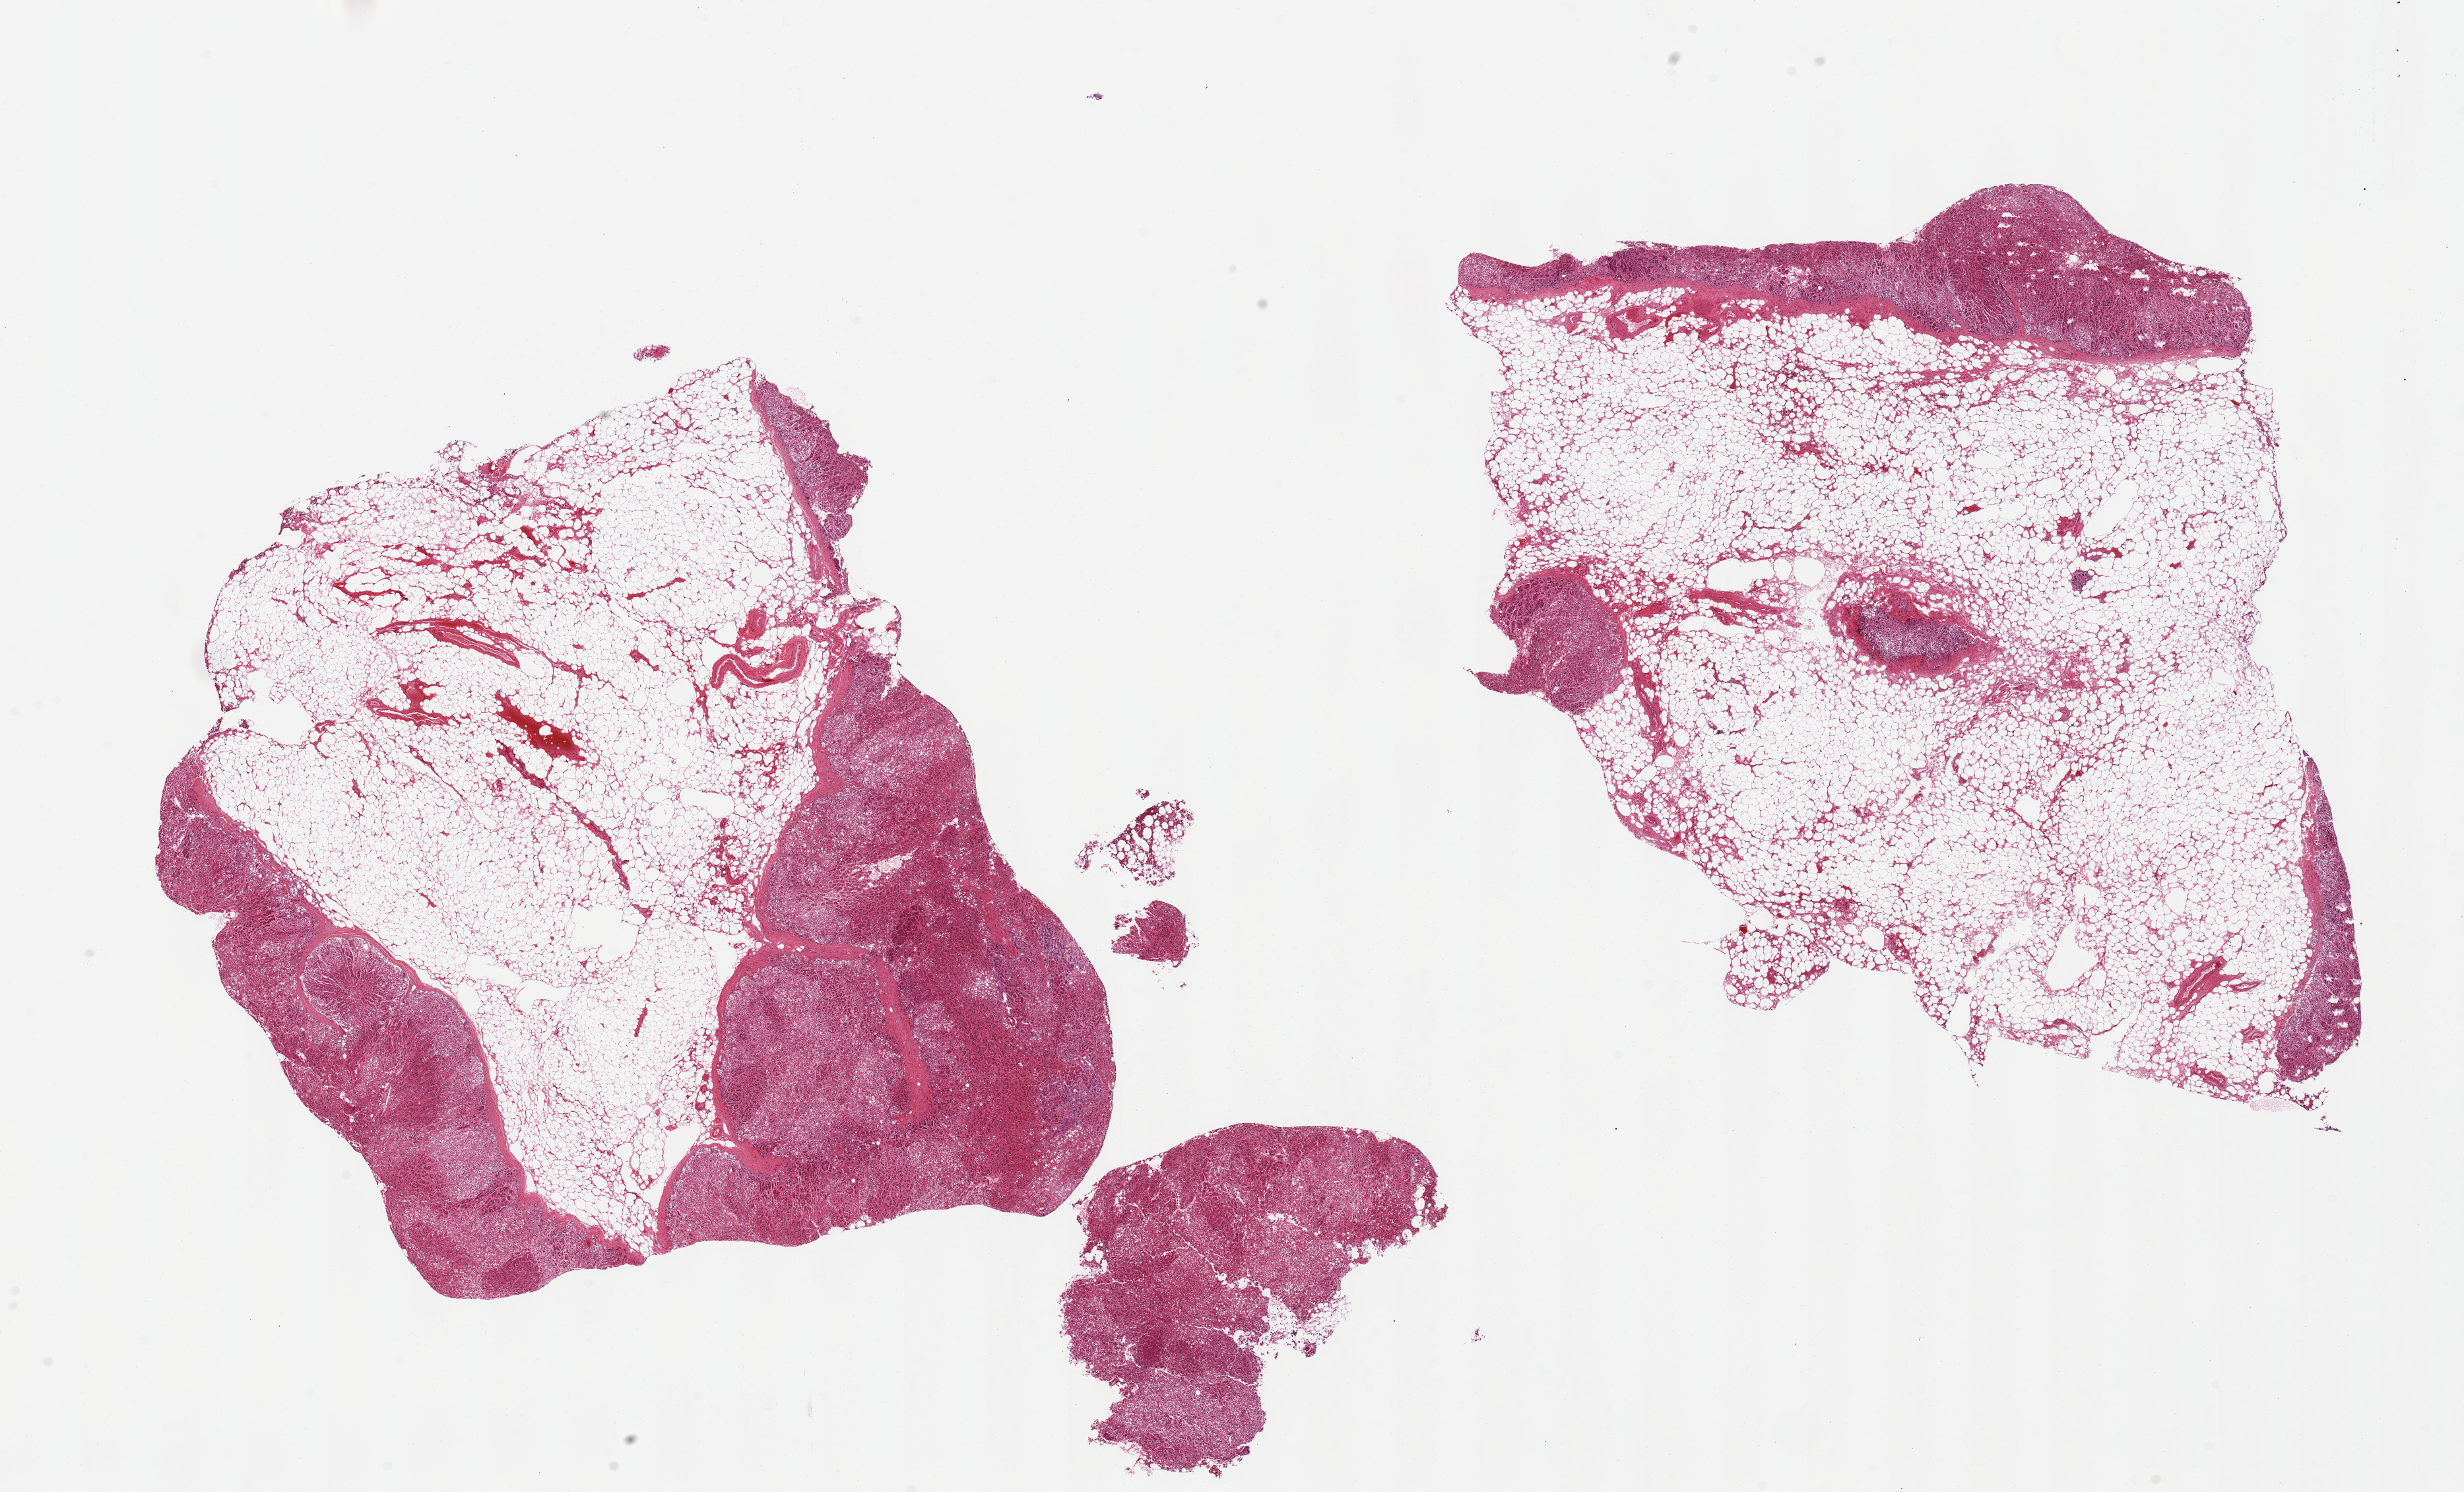
H&E whole-slide image, shown as a low-resolution overview of the whole scanned area (about 29.5 x 17.9 mm). PAXgene-fixed paraffin-embedded (PFPE) section. Sampled site (target tissue): adrenal gland. Donor tissue sample.
* review note (as recorded): 2 pieces, one is 80% fat, 2nd is 60% fat